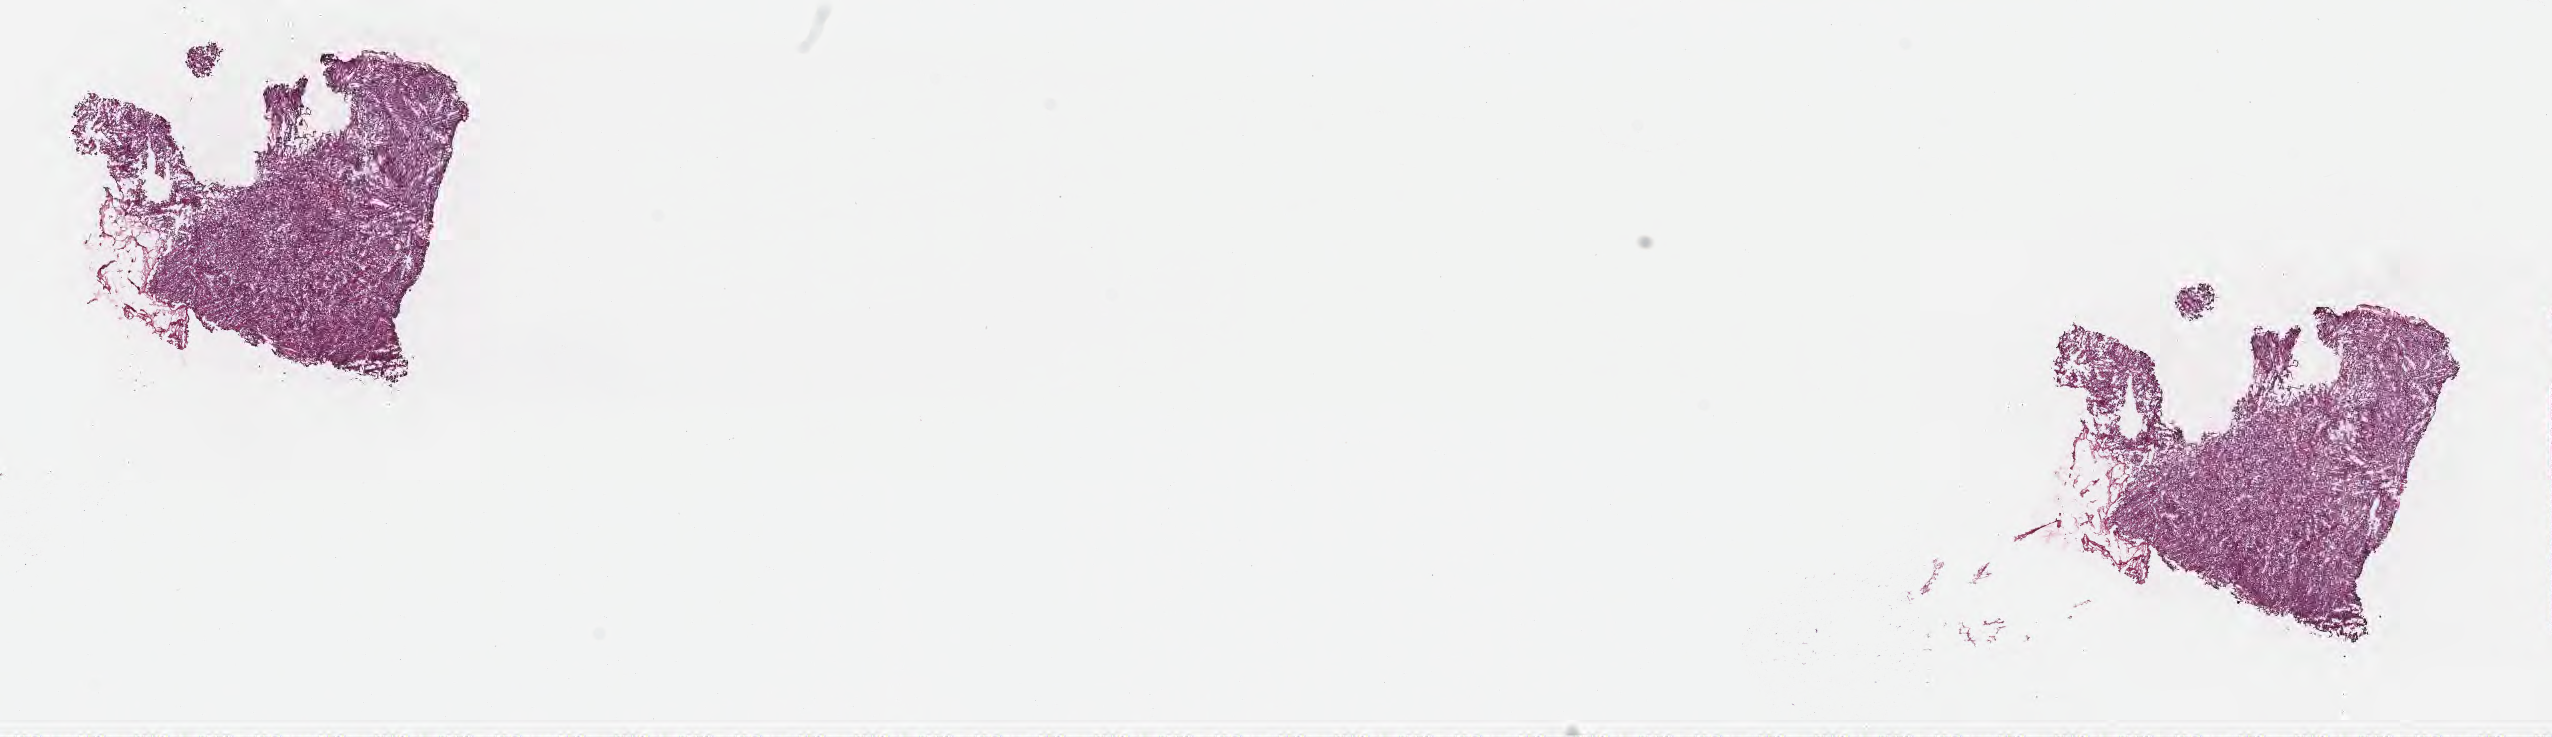
Digitized haematoxylin and eosin-stained section, shown as a low-resolution overview of the whole scanned area (about 20.6 x 6.0 mm); frozen section (tissue freezing medium); primary tumor; site: brain. Female patient; age at initial diagnosis 73 years.
Diagnosis: Glioblastoma, NOS.